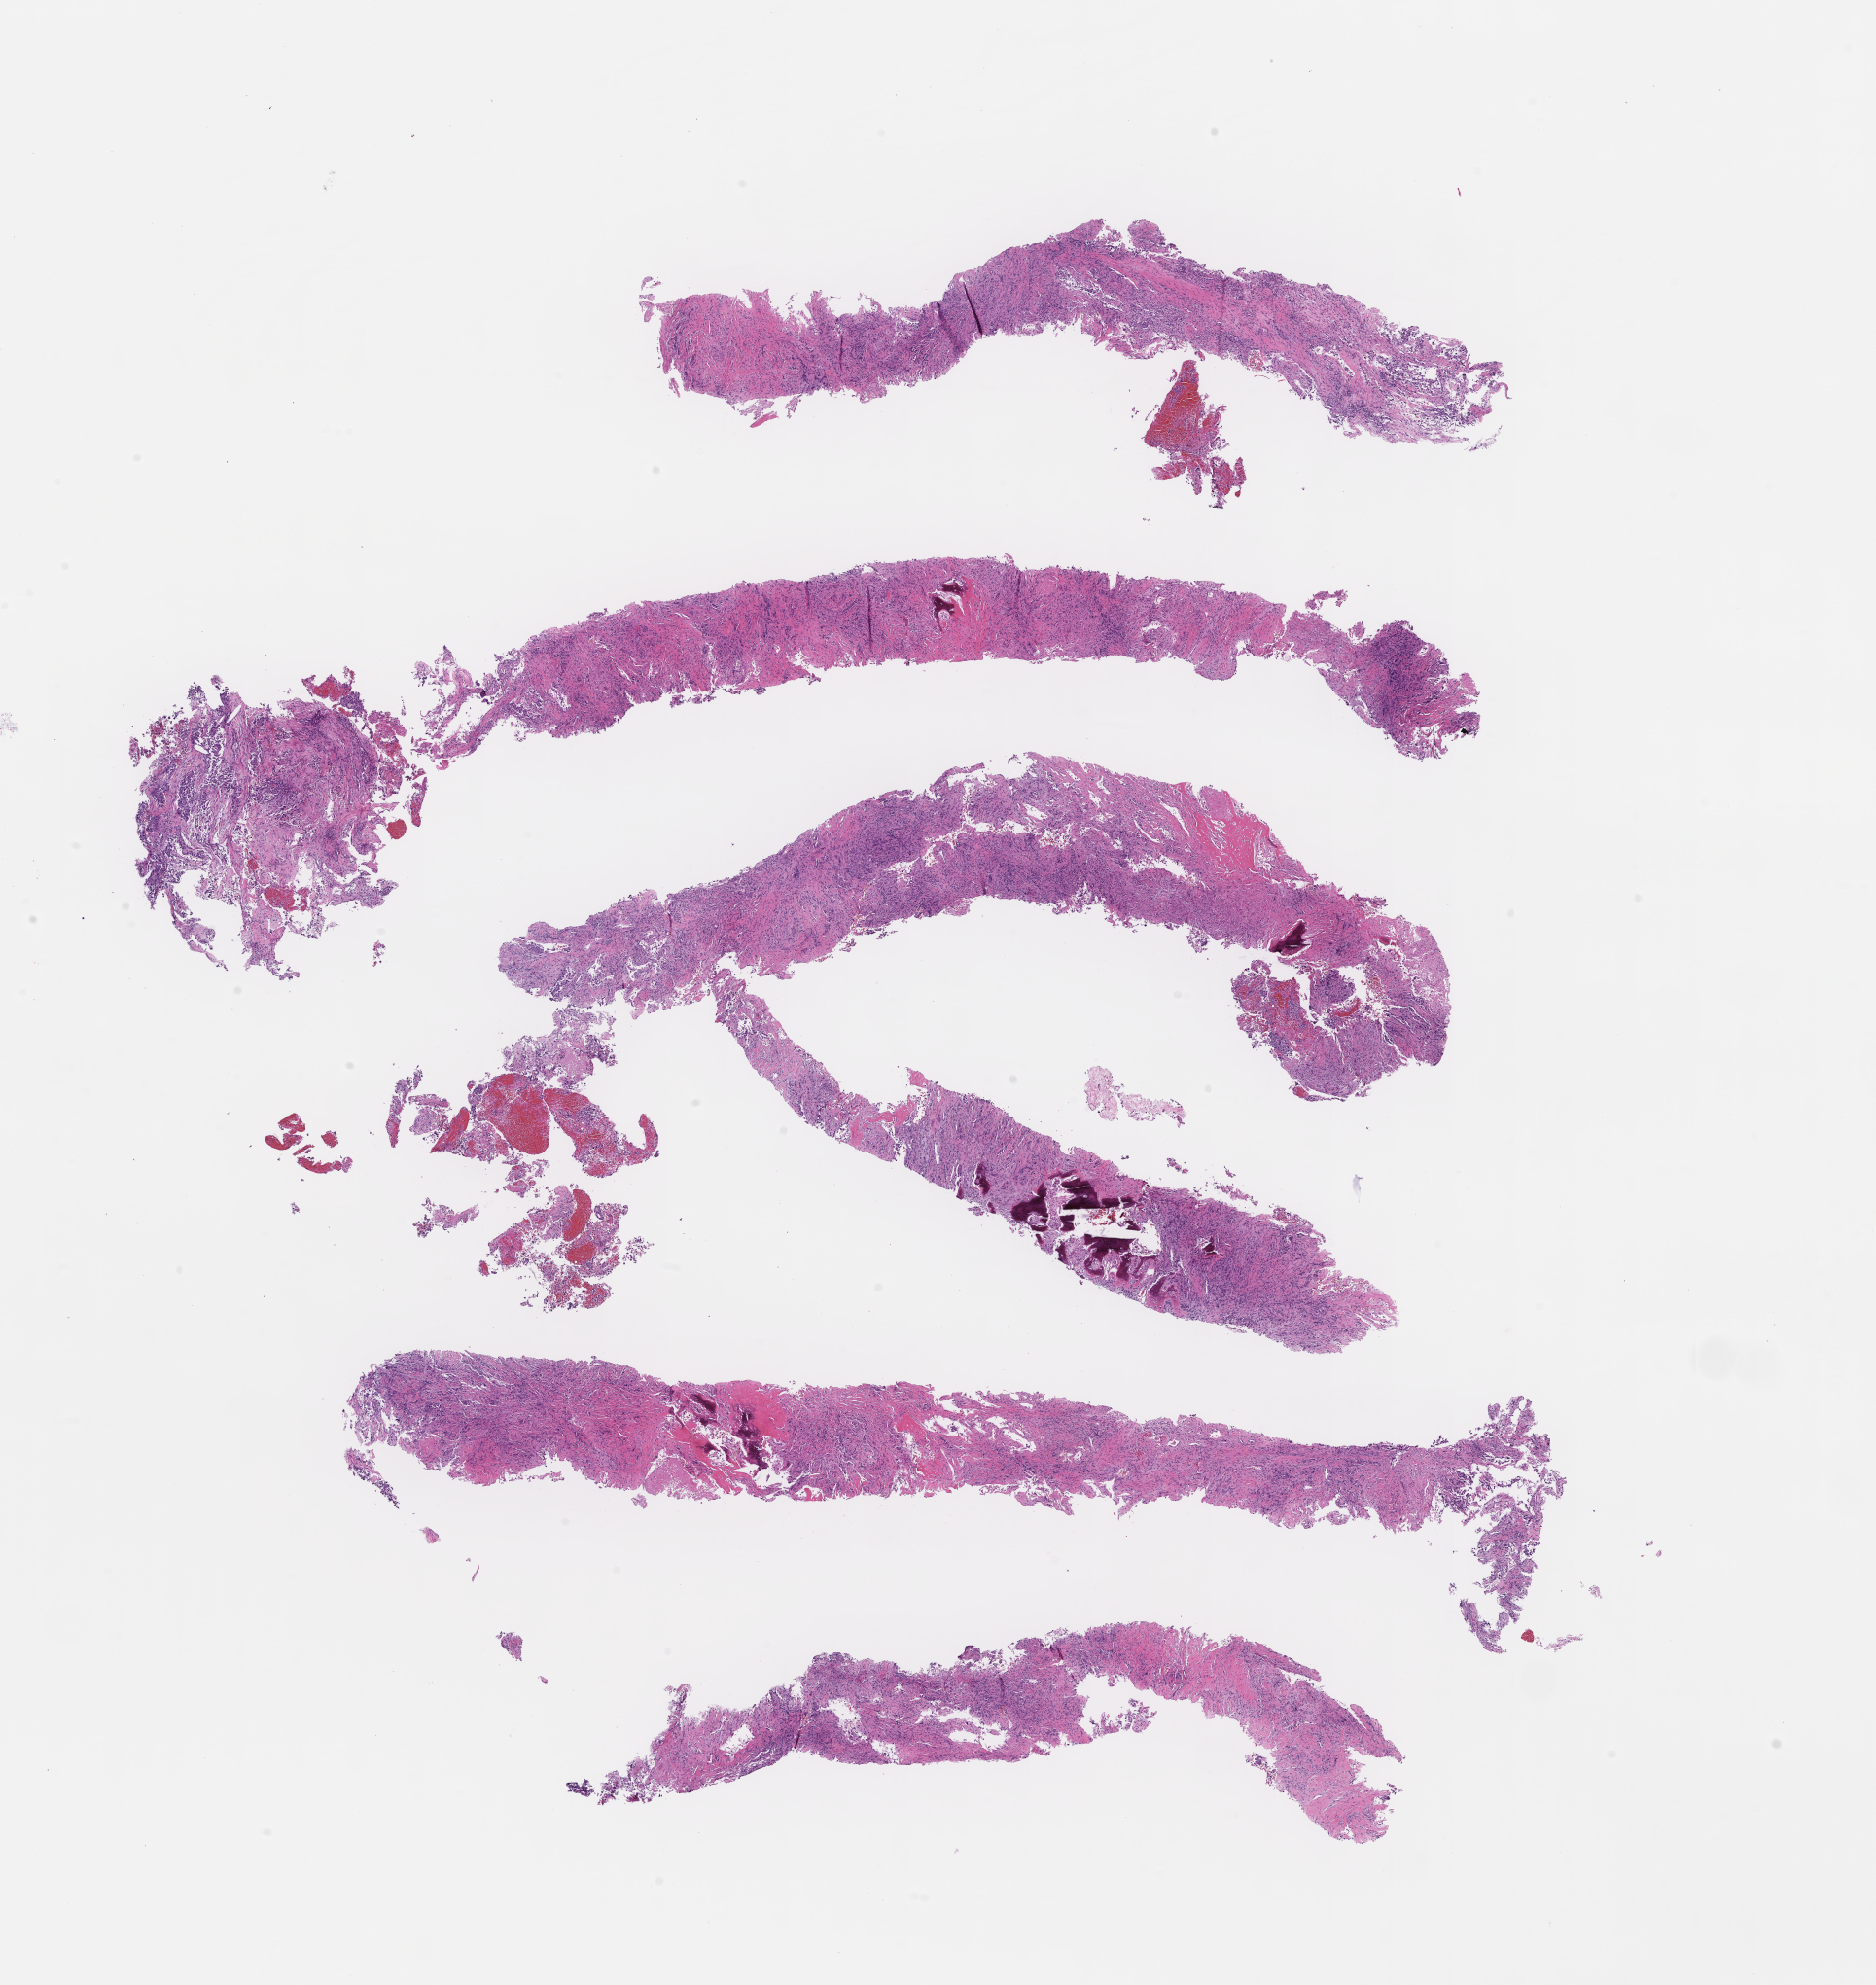
Whole-slide image, haematoxylin and eosin stain, a low-resolution overview of the entire scanned area, about 15.6 x 16.5 mm. FFPE section. Female patient.
This section: metastatic tumor tissue. Primary diagnosis of the patient: Non-Small Cell Lung Carcinoma.